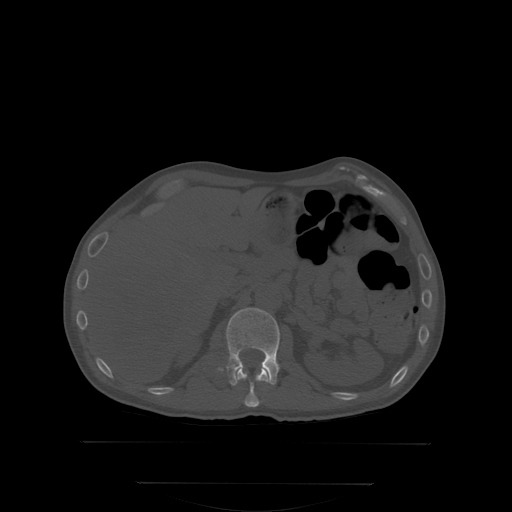
CT including the spine, one axial slice; position 158 of 350 along the scan axis; bone window (W 1800 / L 400 HU); 2.5 mm slice thickness; 512 × 512 image matrix, field of view 500 × 500 mm. Patient: male, 58 years. Case-level facts recorded for this patient, not image findings: primary cancer: prostate; vertebrae with lytic lesions (as recorded): L1.
Outlined on this slice (semi-automatically segmented with operator editing):
- L1 vertebra: box from (x=226, y=307) to (x=291, y=385) px
- T12 vertebra: (x=237, y=366)–(x=269, y=407)